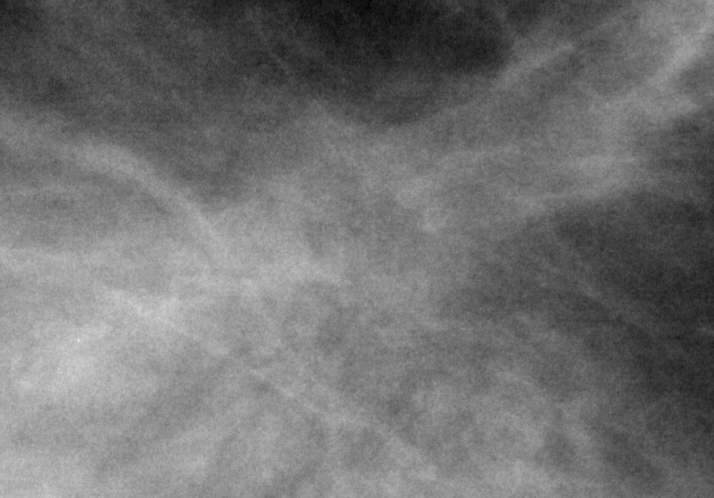
Cropped region of a digitized screen-film mammogram centred on a radiologist-marked abnormality, left breast, MLO view.
- Finding: mass, shape architectural distortion, margins spiculated; BI-RADS assessment category 5; pathology (as recorded): malignant.